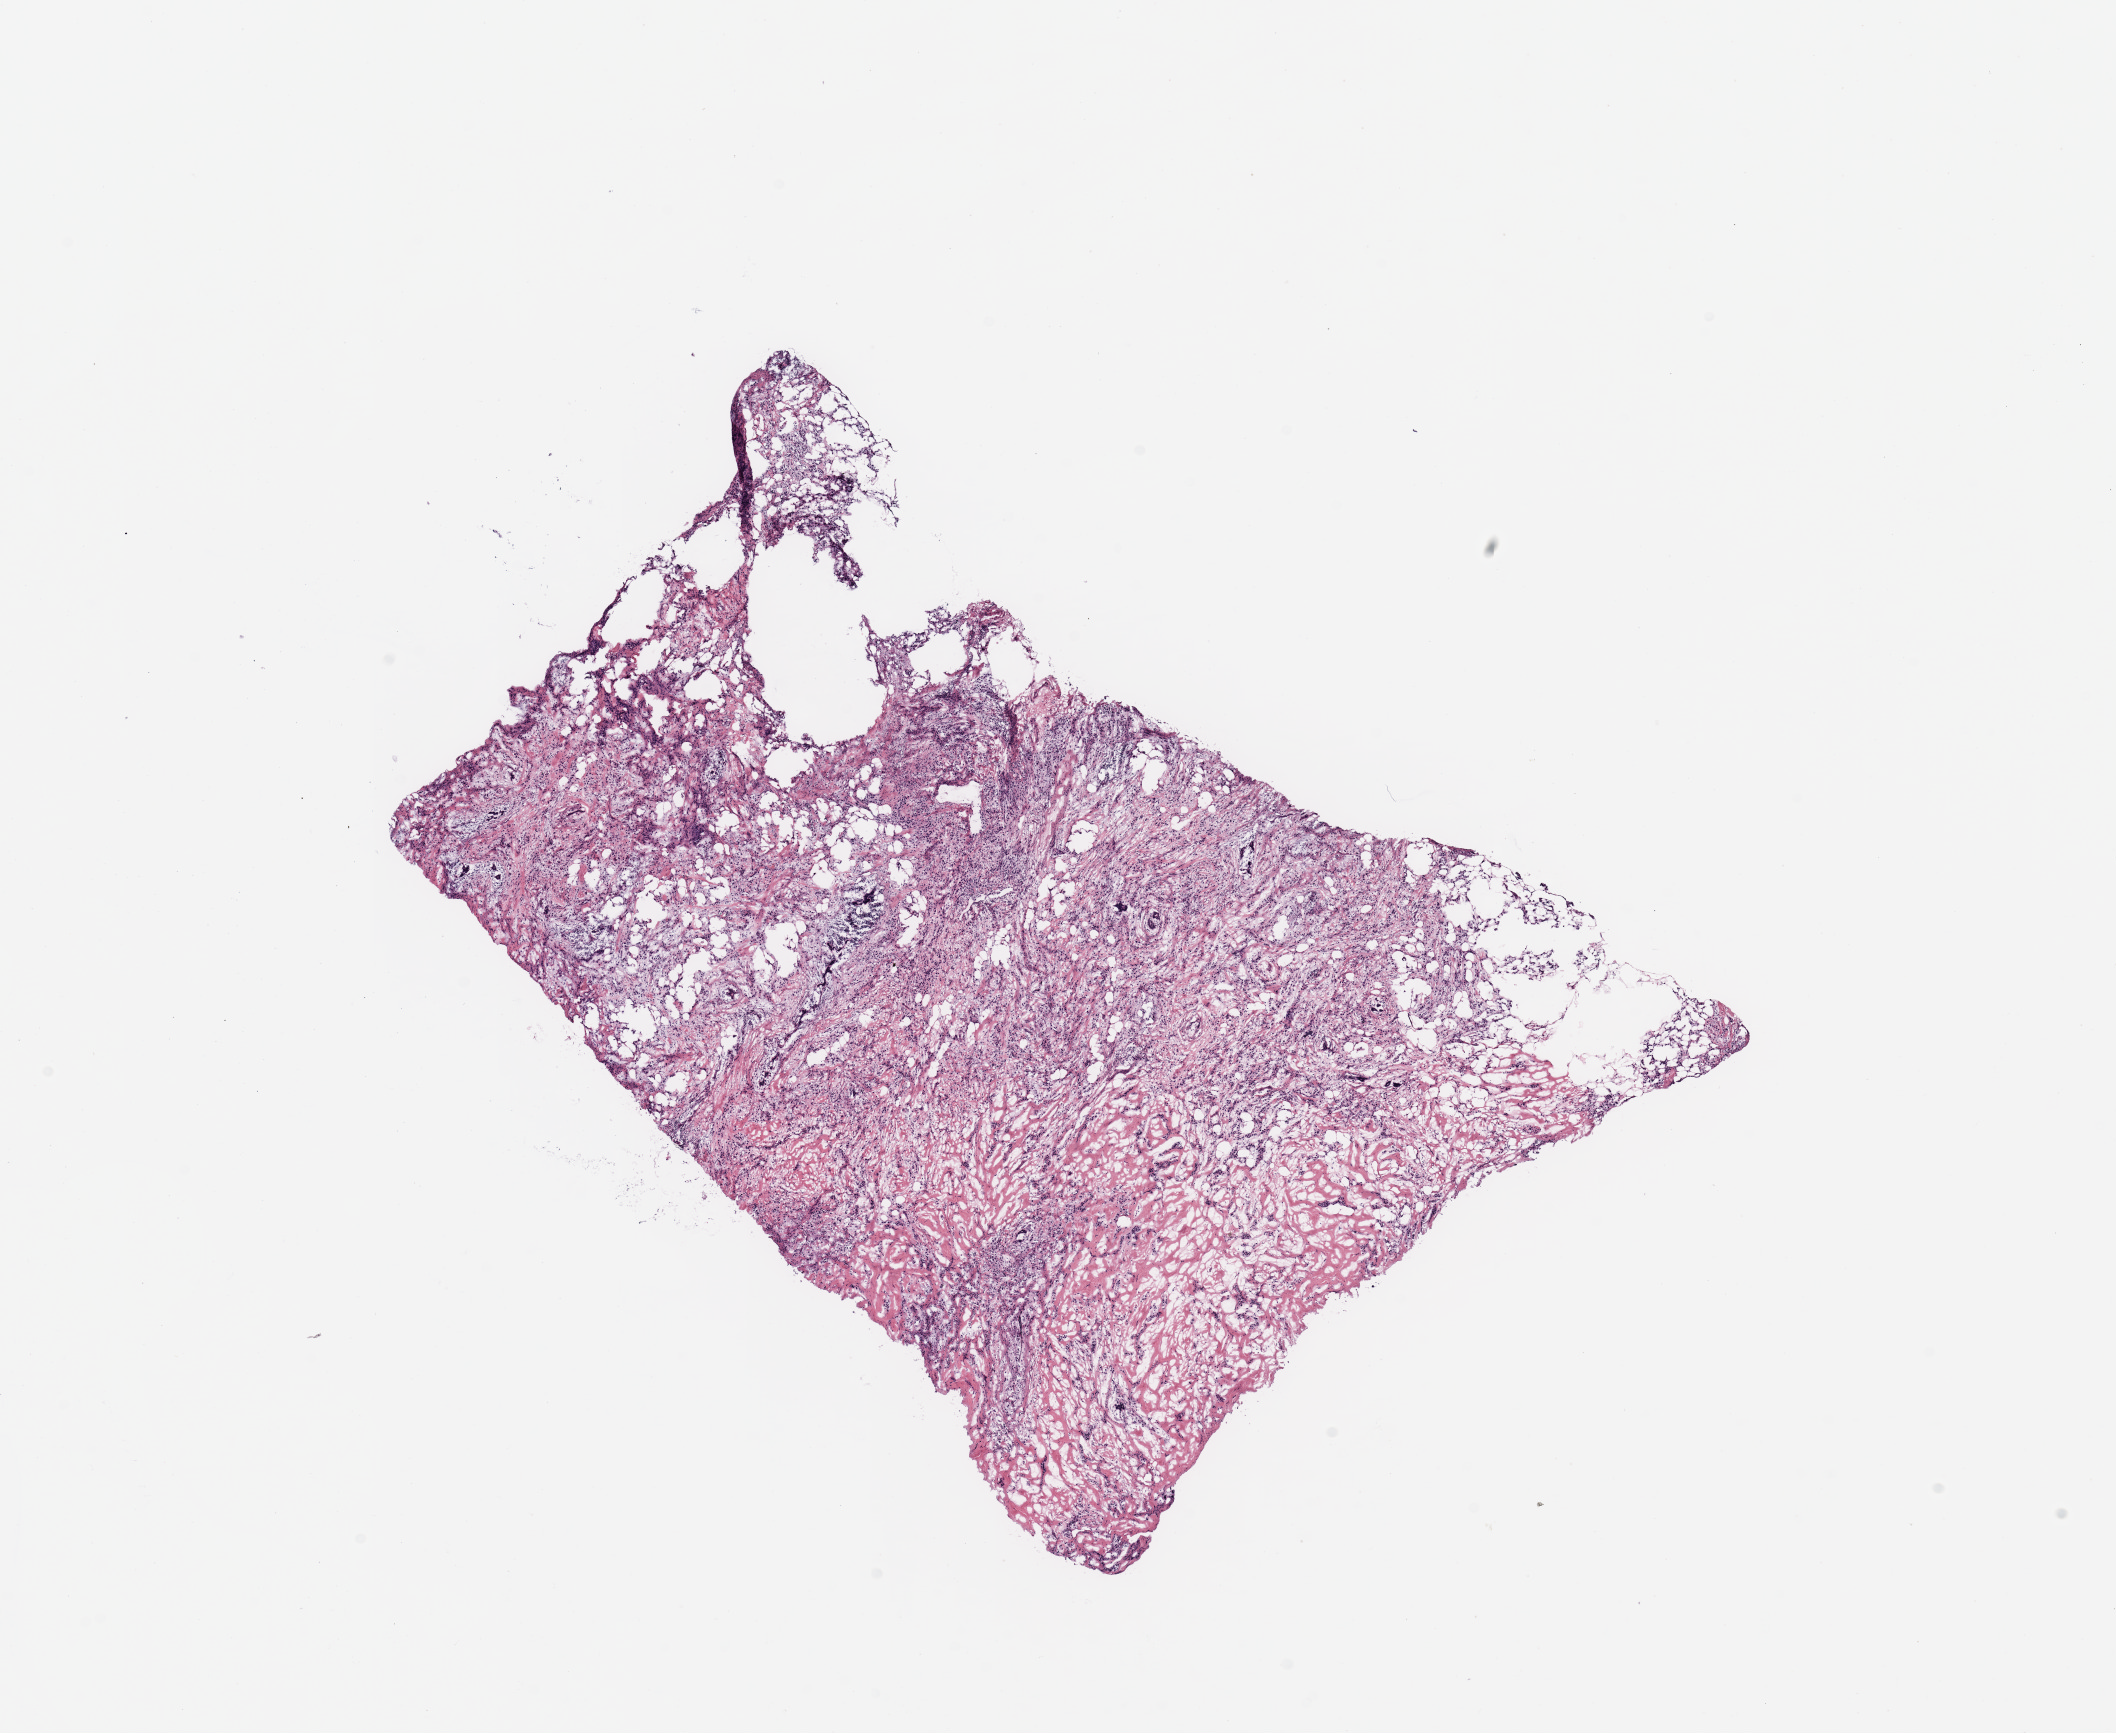
Whole-slide histology image, H&E-stained — whole scanned area (about 16.7 x 13.7 mm, slide scanned at 20x) shown as a low-resolution overview; breast, tissue type not recorded.
Patient diagnosis (cohort enrolment): breast cancer (breast).